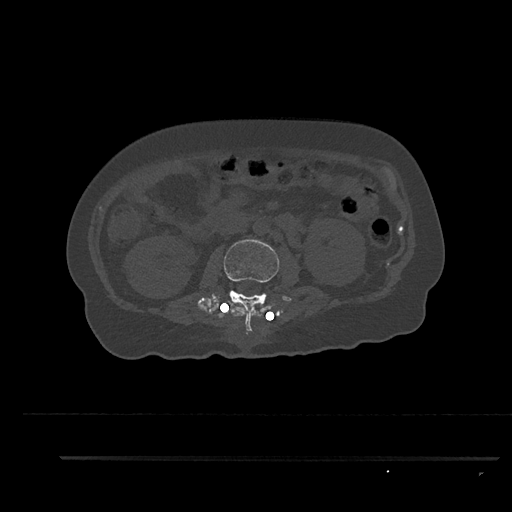
CT including the spine, one axial slice; slice 144 of 797 in the series (ordered by position); bone window (W 1800 / L 400 HU); 512 × 512 image matrix, field of view 408 × 408 mm. Female patient, age 44 years. Case-level facts recorded for this patient, not image findings: primary cancer: renal; vertebrae with lytic lesions (as recorded): L1.
Annotated regions visible in this slice (semi-automatic segmentation, software-assisted and operator-edited):
- L2 vertebra: box from (x=197, y=239) to (x=280, y=335) px